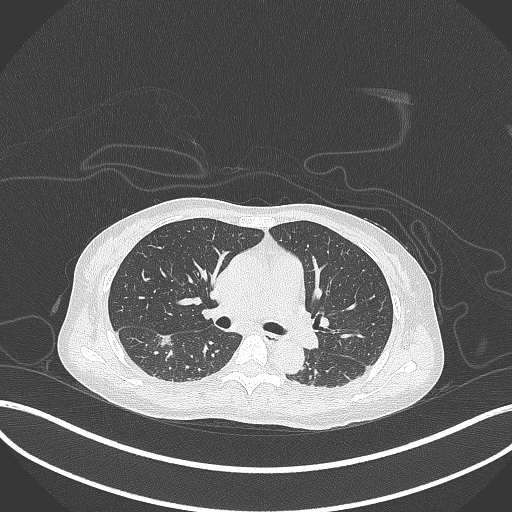
Chest CT, one axial slice. Slice 183 of 261 in the series (ordered by position). 120 kVp. Lung window (W 1500 / L -600 HU). 1 mm slice thickness. 512 × 512 image matrix, field of view 400 × 400 mm. Female patient, age 44 years. From the clinical record (not read from this slice): clinical TNM (as recorded): T1c N0 M0.
Outlined on this slice (rectangle marked by the reading radiologist):
- lung tumour (recorded histology: adenocarcinoma): bounding box (x1, y1, x2, y2) in pixels: (157, 332, 173, 346)